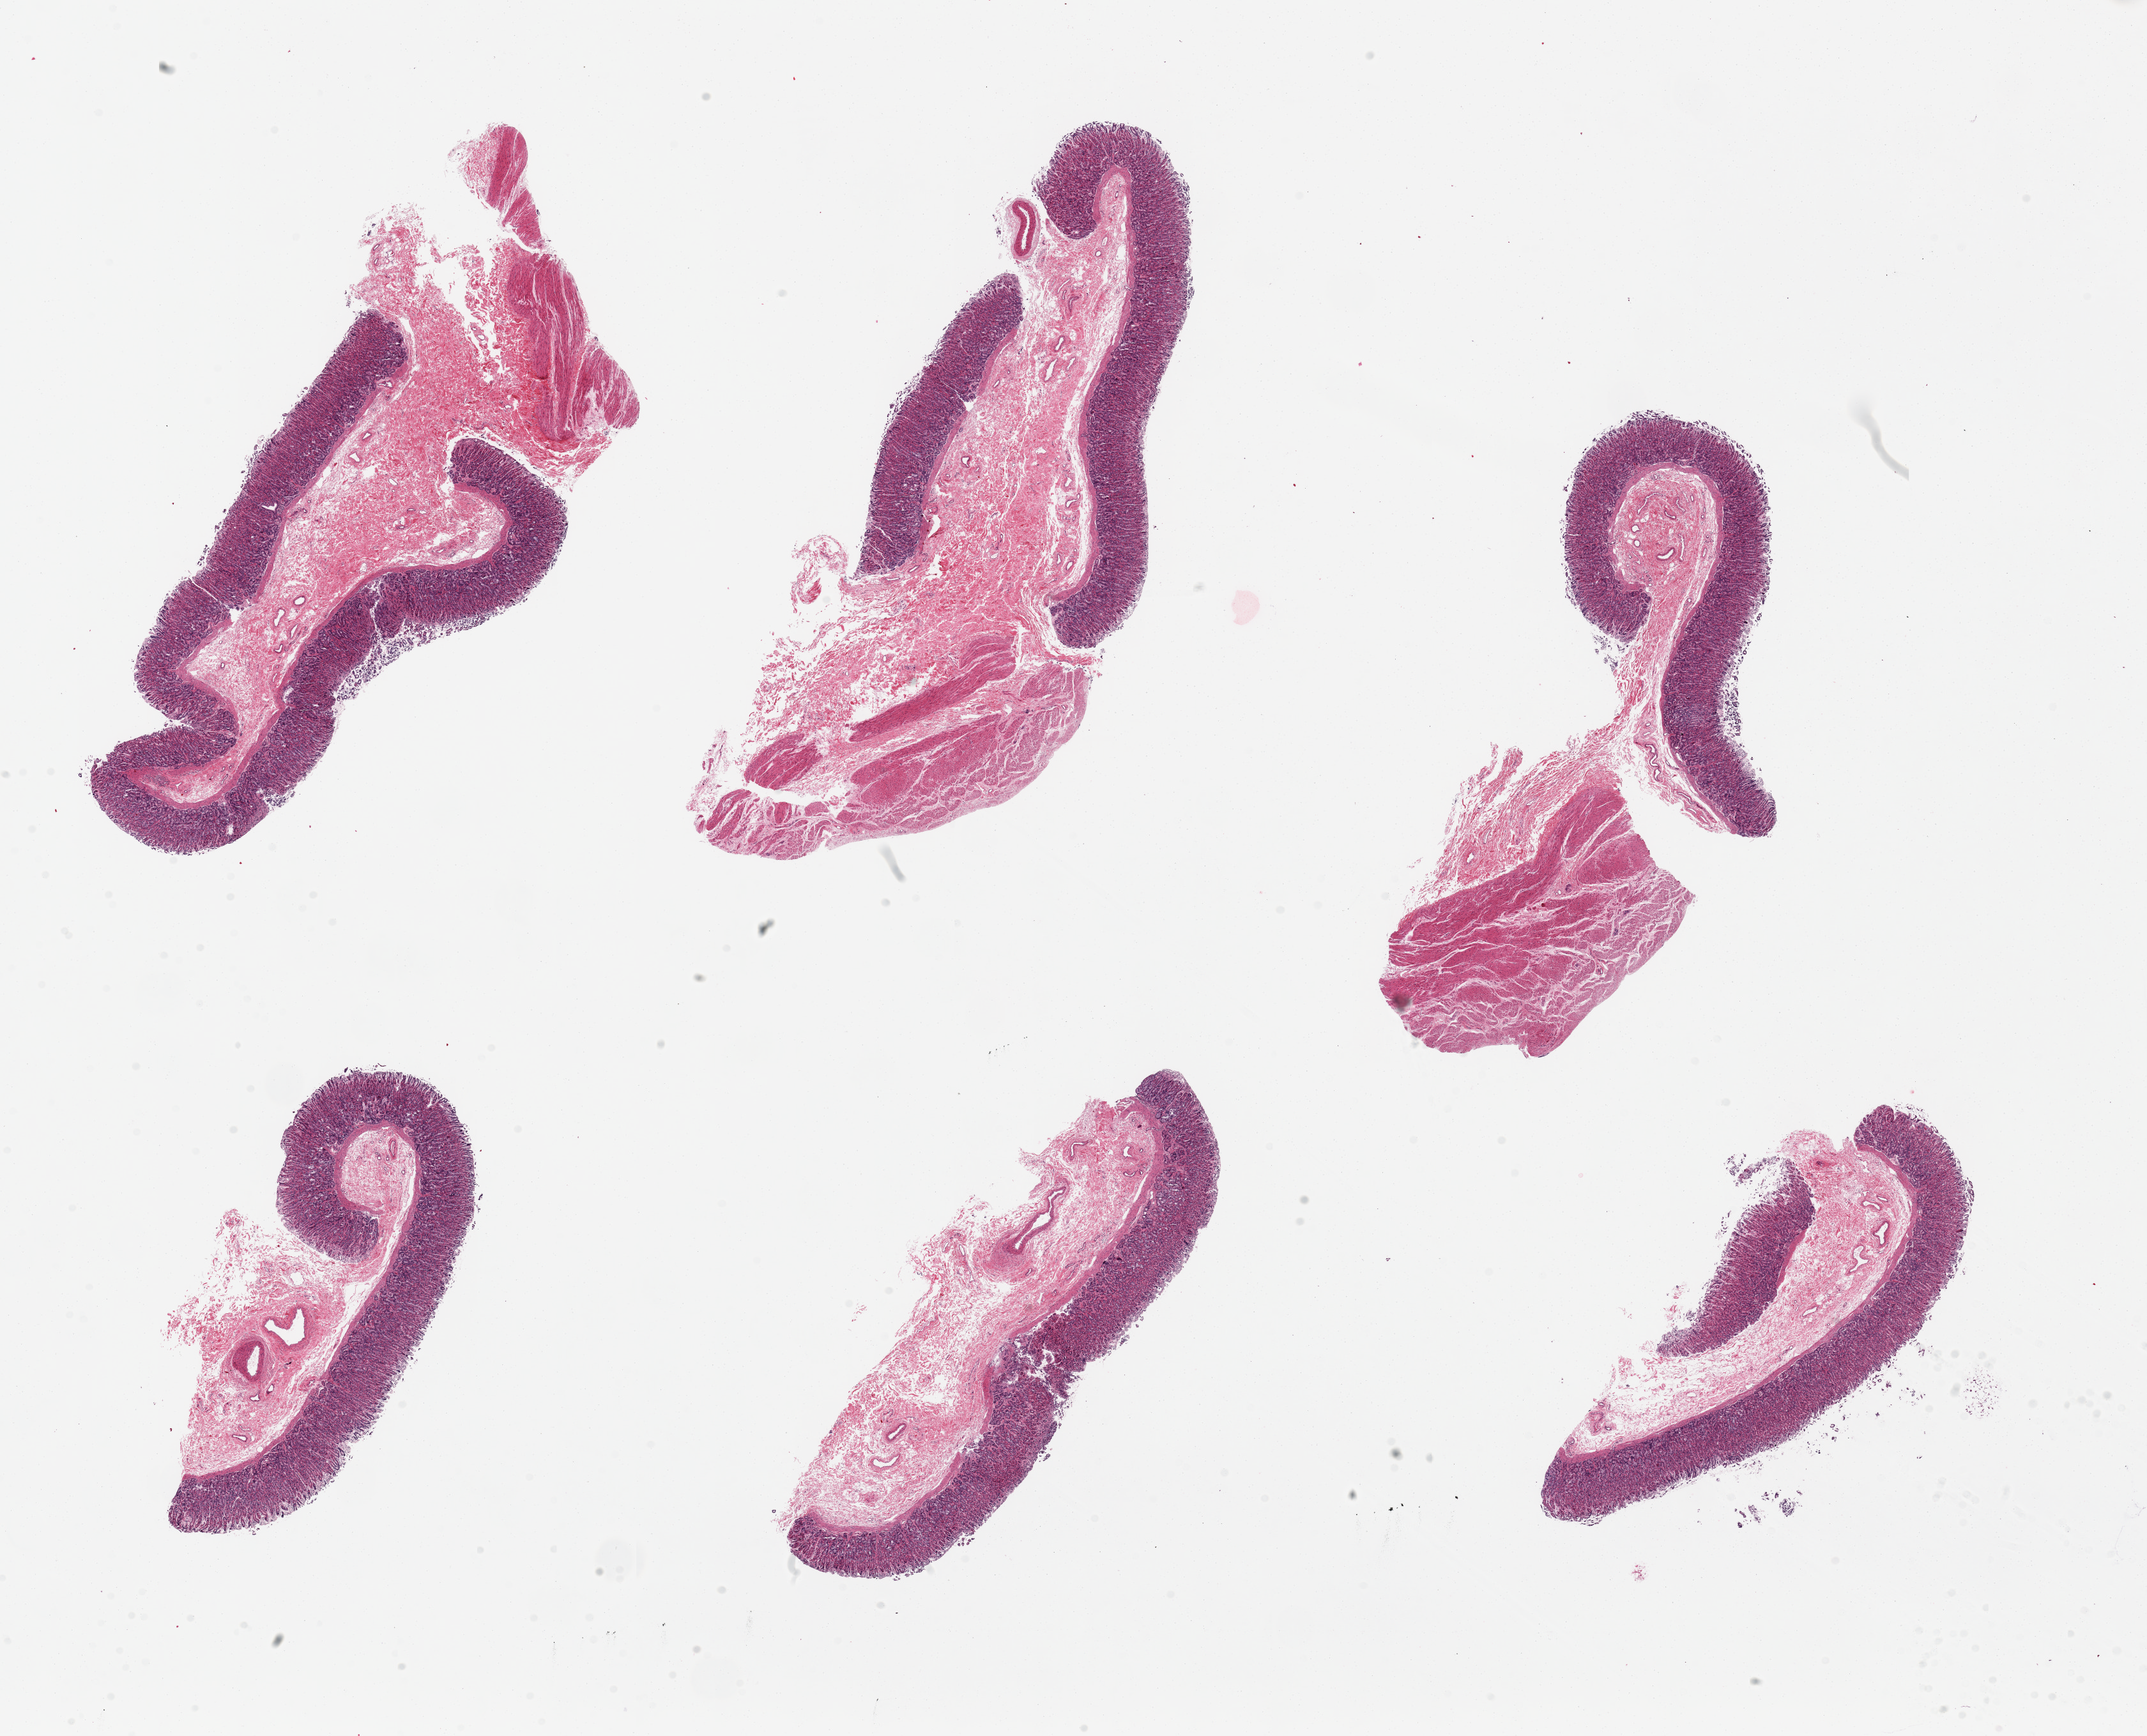
H&E whole-slide image — whole scanned area (about 26.6 x 21.5 mm, slide scanned at 20x) shown as a low-resolution overview. Donor sex: female.
Specimen: PAXgene-fixed, paraffin-embedded tissue; sampled site (target tissue): stomach; tissue donor sample.